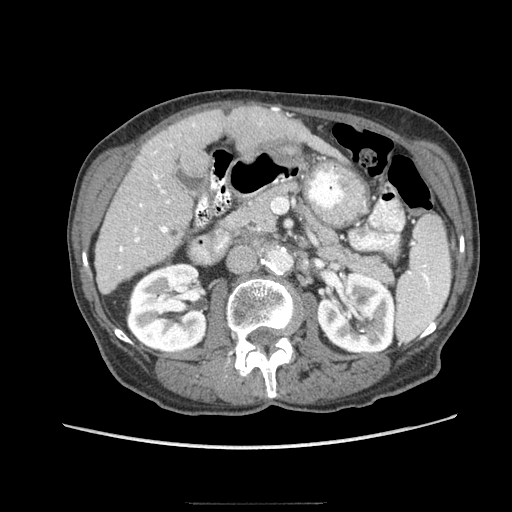
Contrast-enhanced abdominal CT (liver protocol), one axial slice. Position 34 of 83 along the scan axis. Reconstruction kernel STANDARD. 140 kVp. Soft-tissue window (W 400 / L 40 HU). 2.5 mm slice thickness. 512 × 512 image matrix, field of view 360 × 360 mm. Case-level facts recorded for this patient, not image findings: diagnosis: hepatocellular carcinoma (patient treated with transarterial chemoembolisation; whether this scan precedes or follows treatment is not stated here); TNM stage (as recorded): Stage-I.
Structures marked on this image (semi-automatically segmented with operator editing):
- liver parenchyma outside the tumour (the mass and vessels are separate outlines, so this box may not span the whole liver): bounding box (x1, y1, x2, y2) in pixels: (94, 106, 304, 293)
- liver vessels: (117, 123, 195, 269)